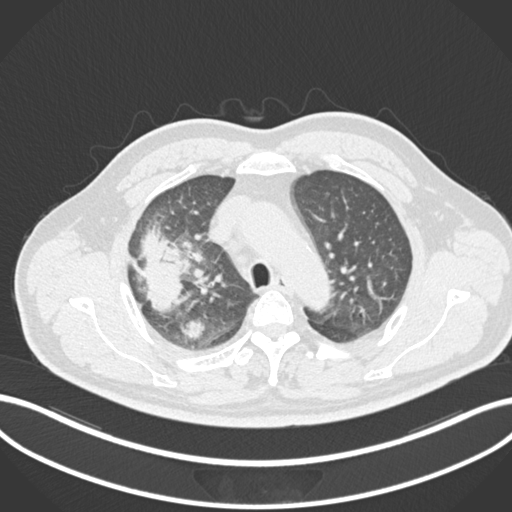
Chest CT, one axial slice; position 673 of 852 along the scan axis; reconstruction kernel B30f; 120 kVp; lung window (W 1500 / L -600 HU); 1 mm slice thickness; 512 × 512 image matrix. Patient: male, 55 years. From the clinical record (not read from this slice): clinical TNM (as recorded): T3 N2 M1.
Structures marked on this image (bounding box drawn by a radiologist):
- lung tumour (recorded histology: adenocarcinoma): box from (x=132, y=221) to (x=187, y=316) px